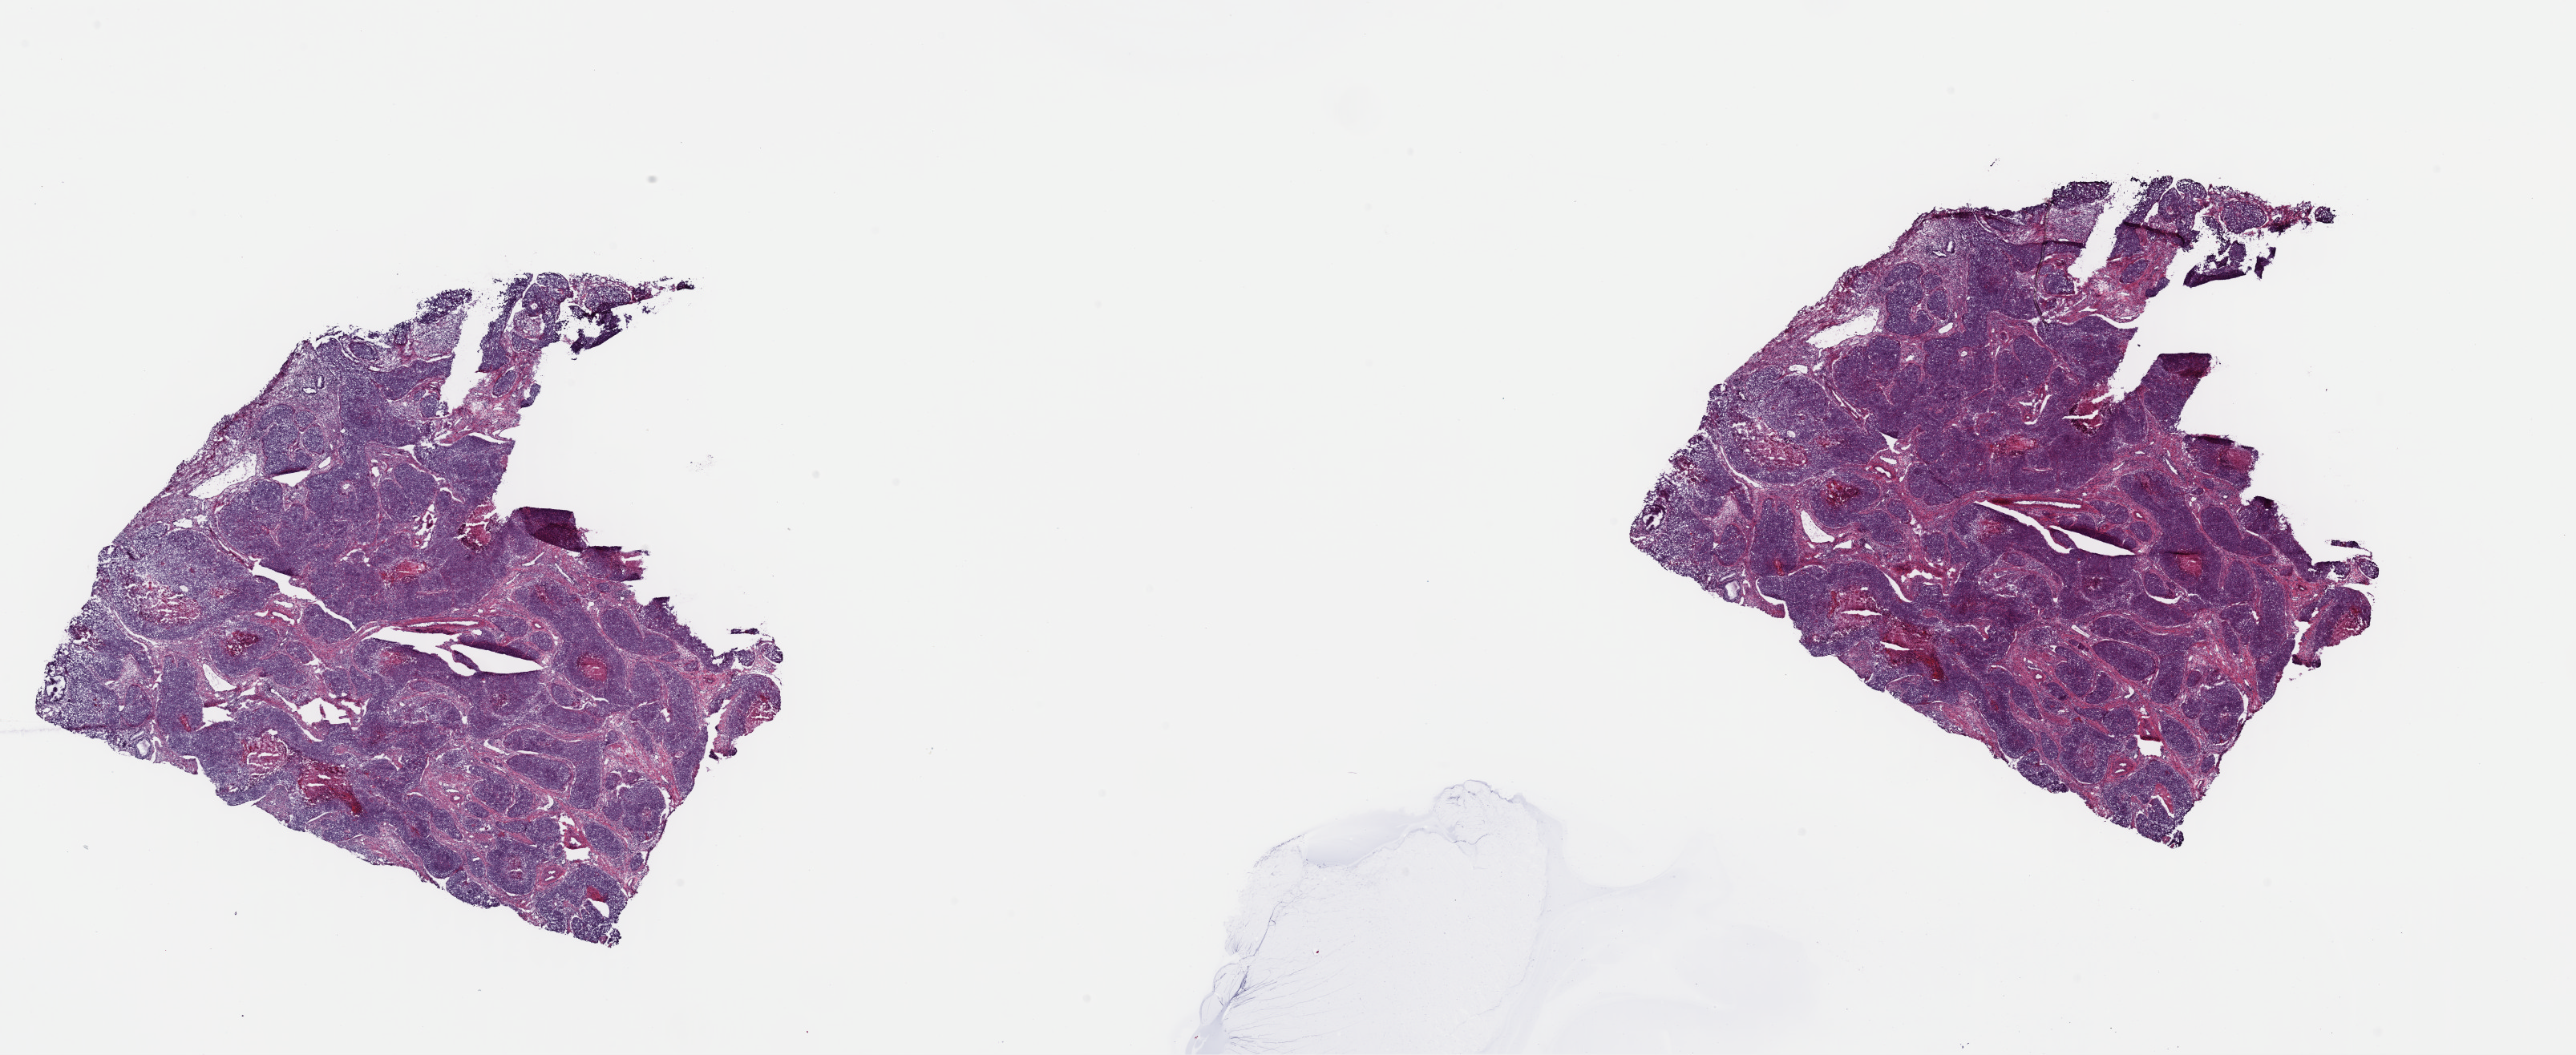
Hematoxylin and eosin (H&E) stained whole-slide image, a low-resolution overview of the entire scanned area, about 25.4 x 10.4 mm; frozen section from the top of the tissue portion; cervix, primary tumour sample. Female patient; age at initial diagnosis 35 years. Histologic grade: G1 (well differentiated). Composition of this section per pathologist review: tumour cells 90%, tumour nuclei 90%, normal cells 0%, stromal cells 0%, necrosis 10%. Infiltration values recorded for this section: lymphocyte infiltration 2%, monocyte infiltration 2%, neutrophil infiltration 1%.
Lymph nodes positive (case pathology): 0 of 10 examined. FIGO stage: IB. Pathologic diagnosis: Squamous cell carcinoma, NOS (cervix uteri).